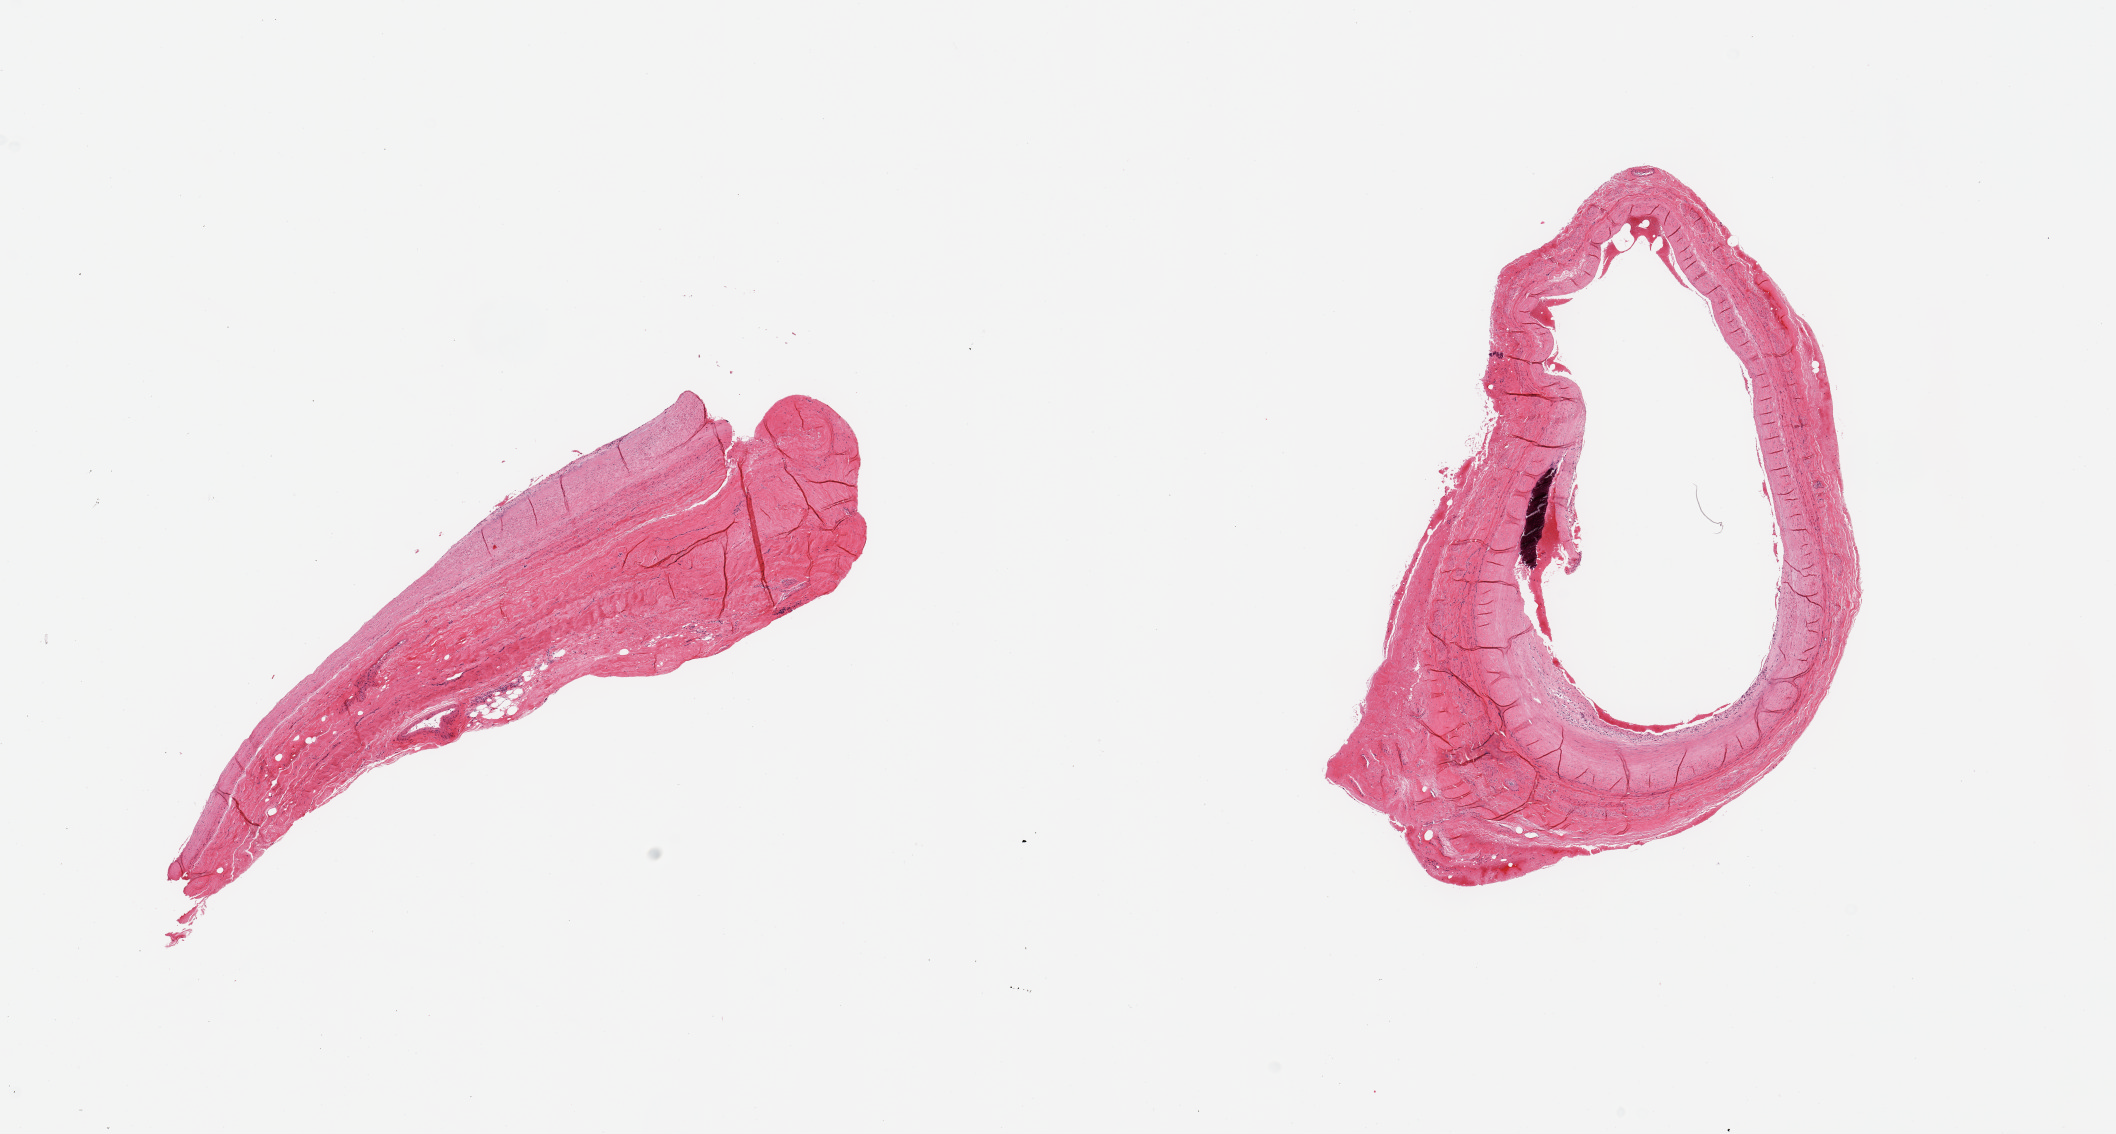
Digitized hematoxylin and eosin (H&E)-stained section — whole scanned area (about 16.7 x 9.0 mm) shown as a low-resolution overview, PAXgene-fixed, paraffin-embedded tissue, section of coronary artery (target tissue), donor tissue sample.
• reviewer comment on this tissue sample: 2 pieces; eccentric sclerotic plaques; 1 piece is longitudinally cut, other is a cross section